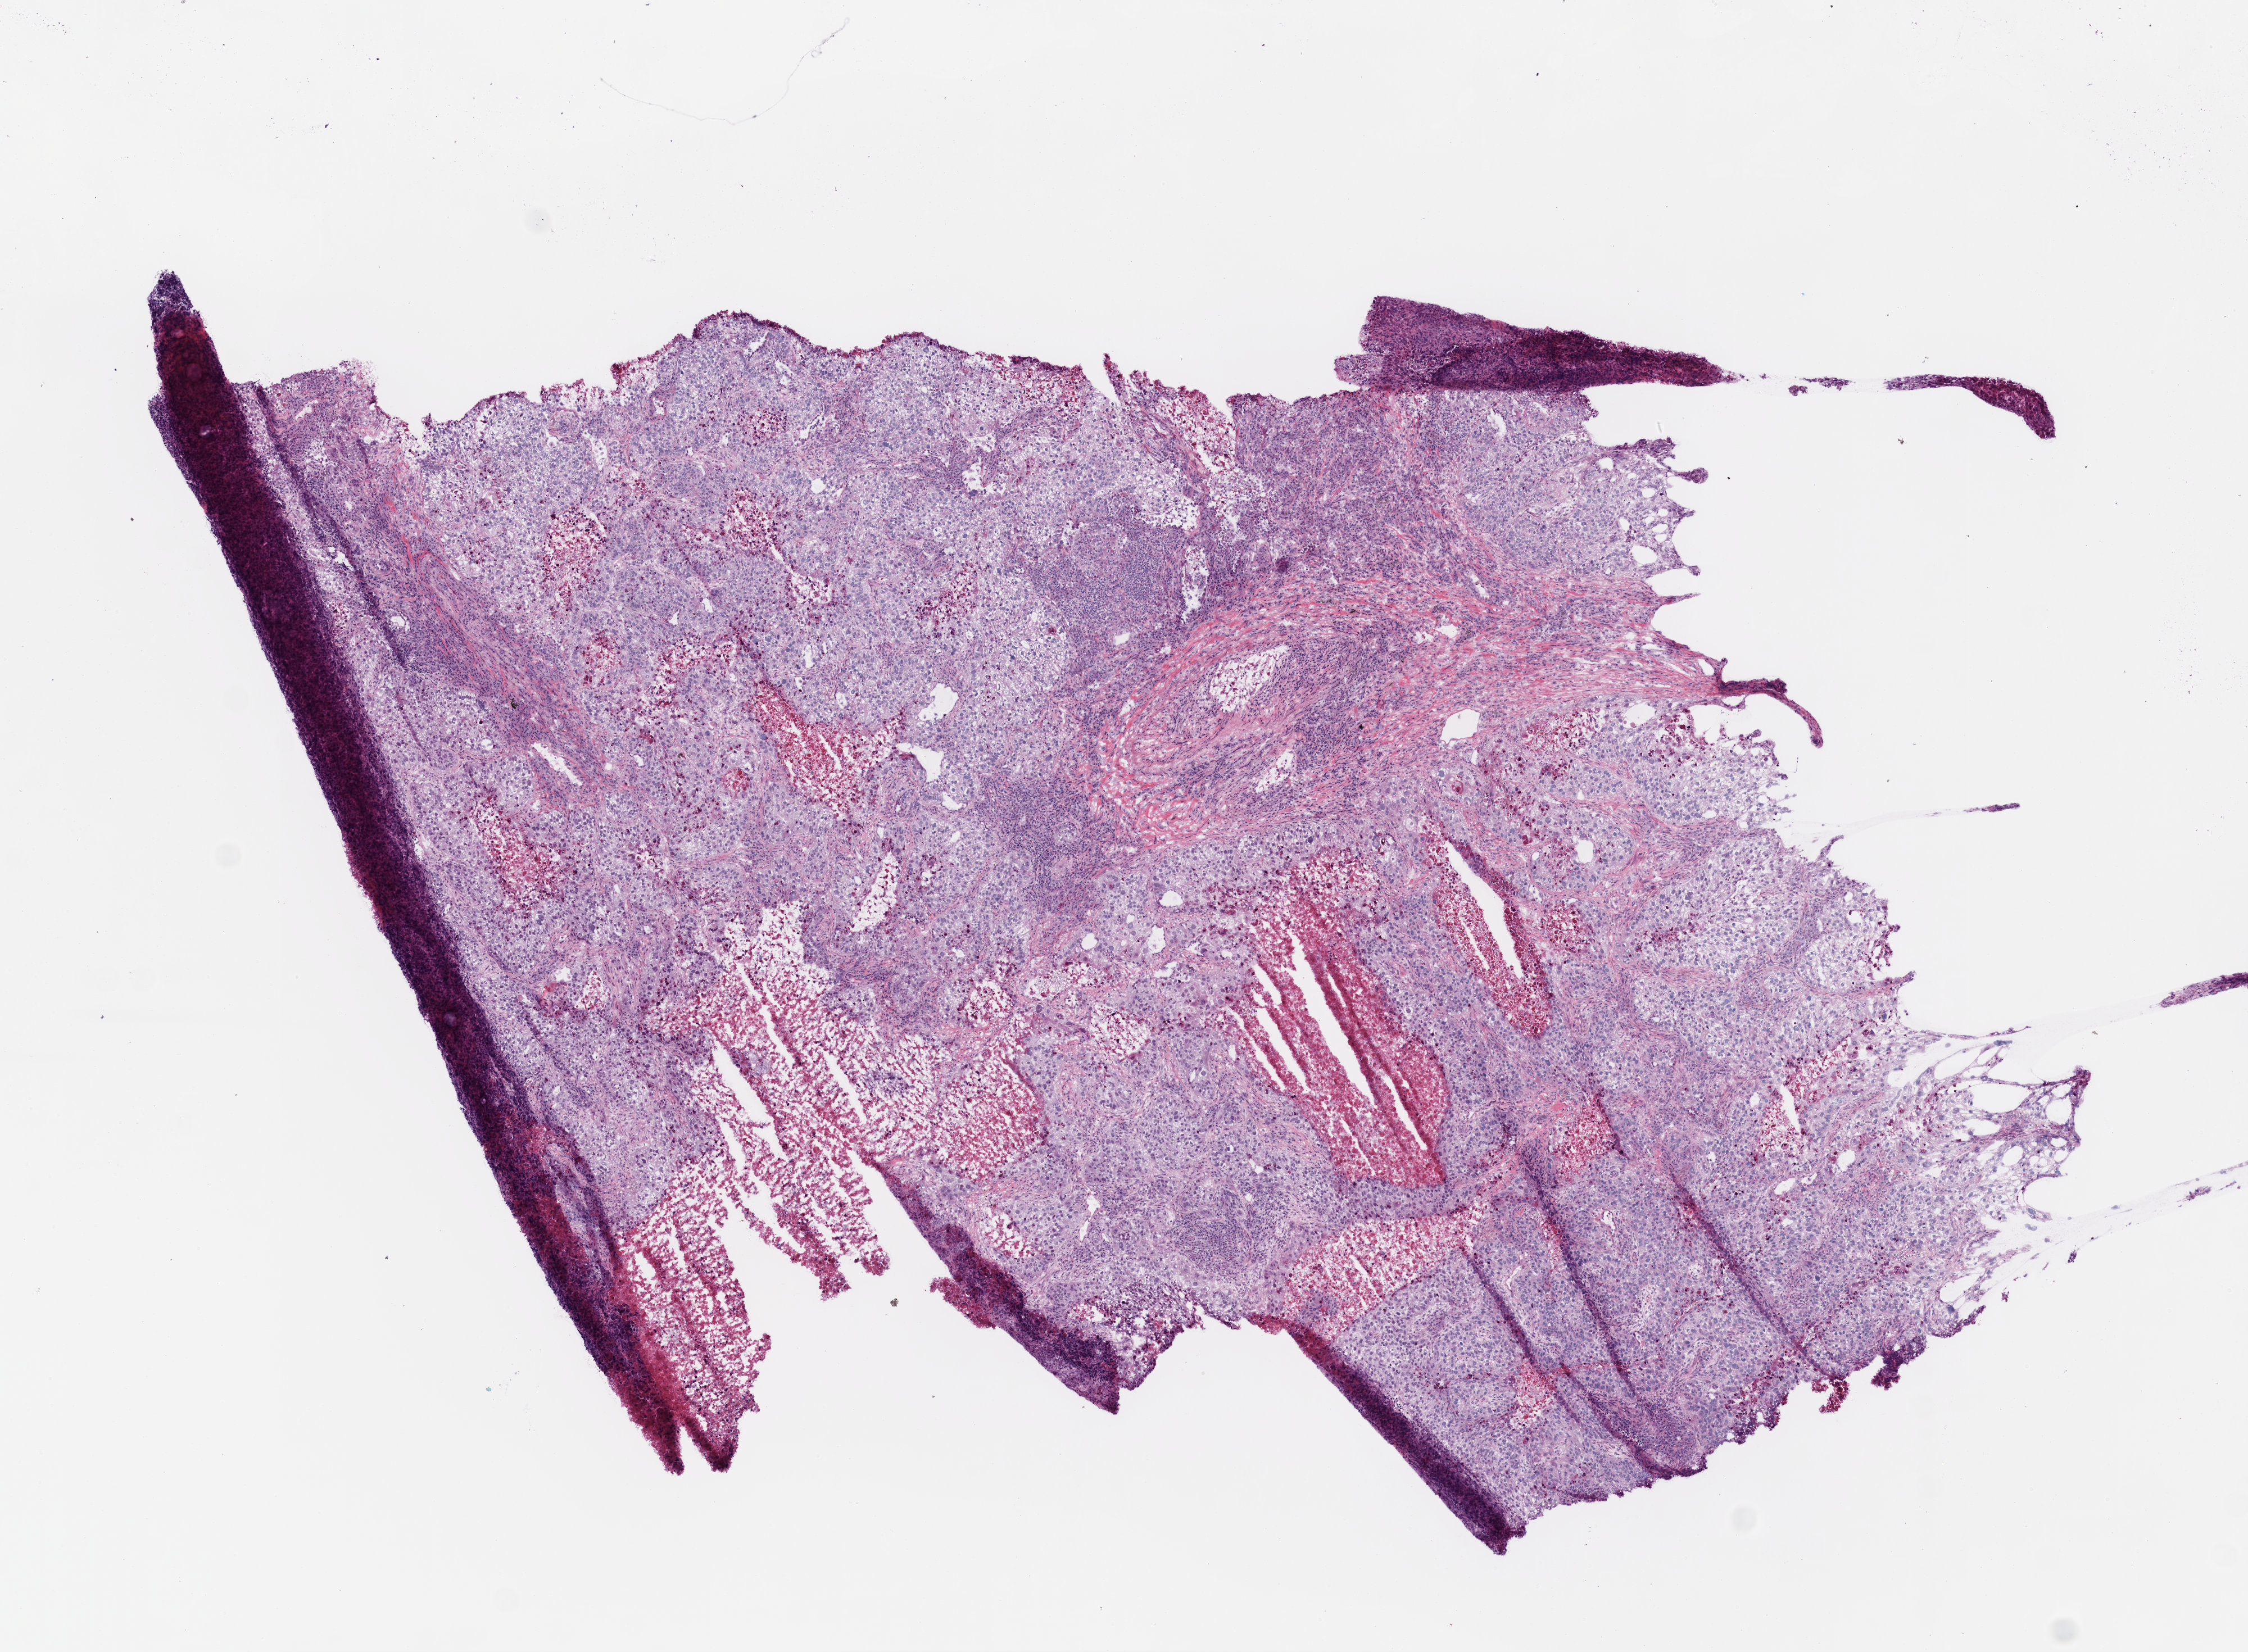
Digitized Hematoxylin and eosin (H&E) stained tissue section (whole slide) — whole scanned area (about 8.0 x 5.9 mm) shown as a low-resolution overview; frozen section from the top of the tissue portion; lung, primary tumour sample. Patient: female, age at initial diagnosis 59 years. Slide review estimates, as recorded: tumour cells 85%, tumour nuclei 75%.
Diagnosis: Squamous cell carcinoma, NOS (upper lobe, lung).